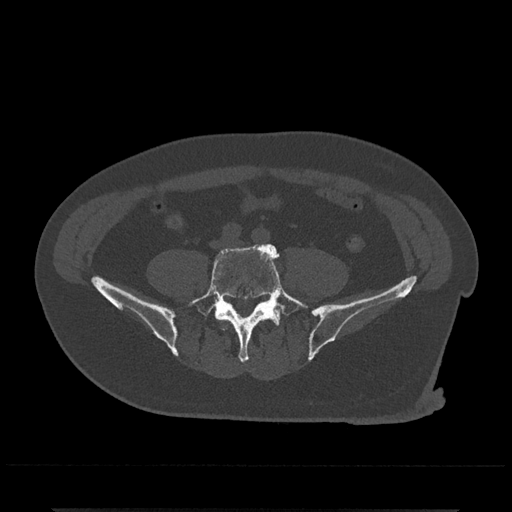
CT including the spine, one axial slice; position 88 of 797 along the scan axis; 120 kVp; bone window (W 1800 / L 400 HU); 0.5 mm slice thickness; 512 × 512 image matrix, field of view 393 × 393 mm. Male patient, age 67 years. From the clinical record (not read from this slice): primary cancer: prostate.
Outlined on this slice (semi-automatic segmentation, software-assisted and operator-edited):
- L5 vertebra: bounding box [x1, y1, x2, y2] px = [186, 243, 309, 363]